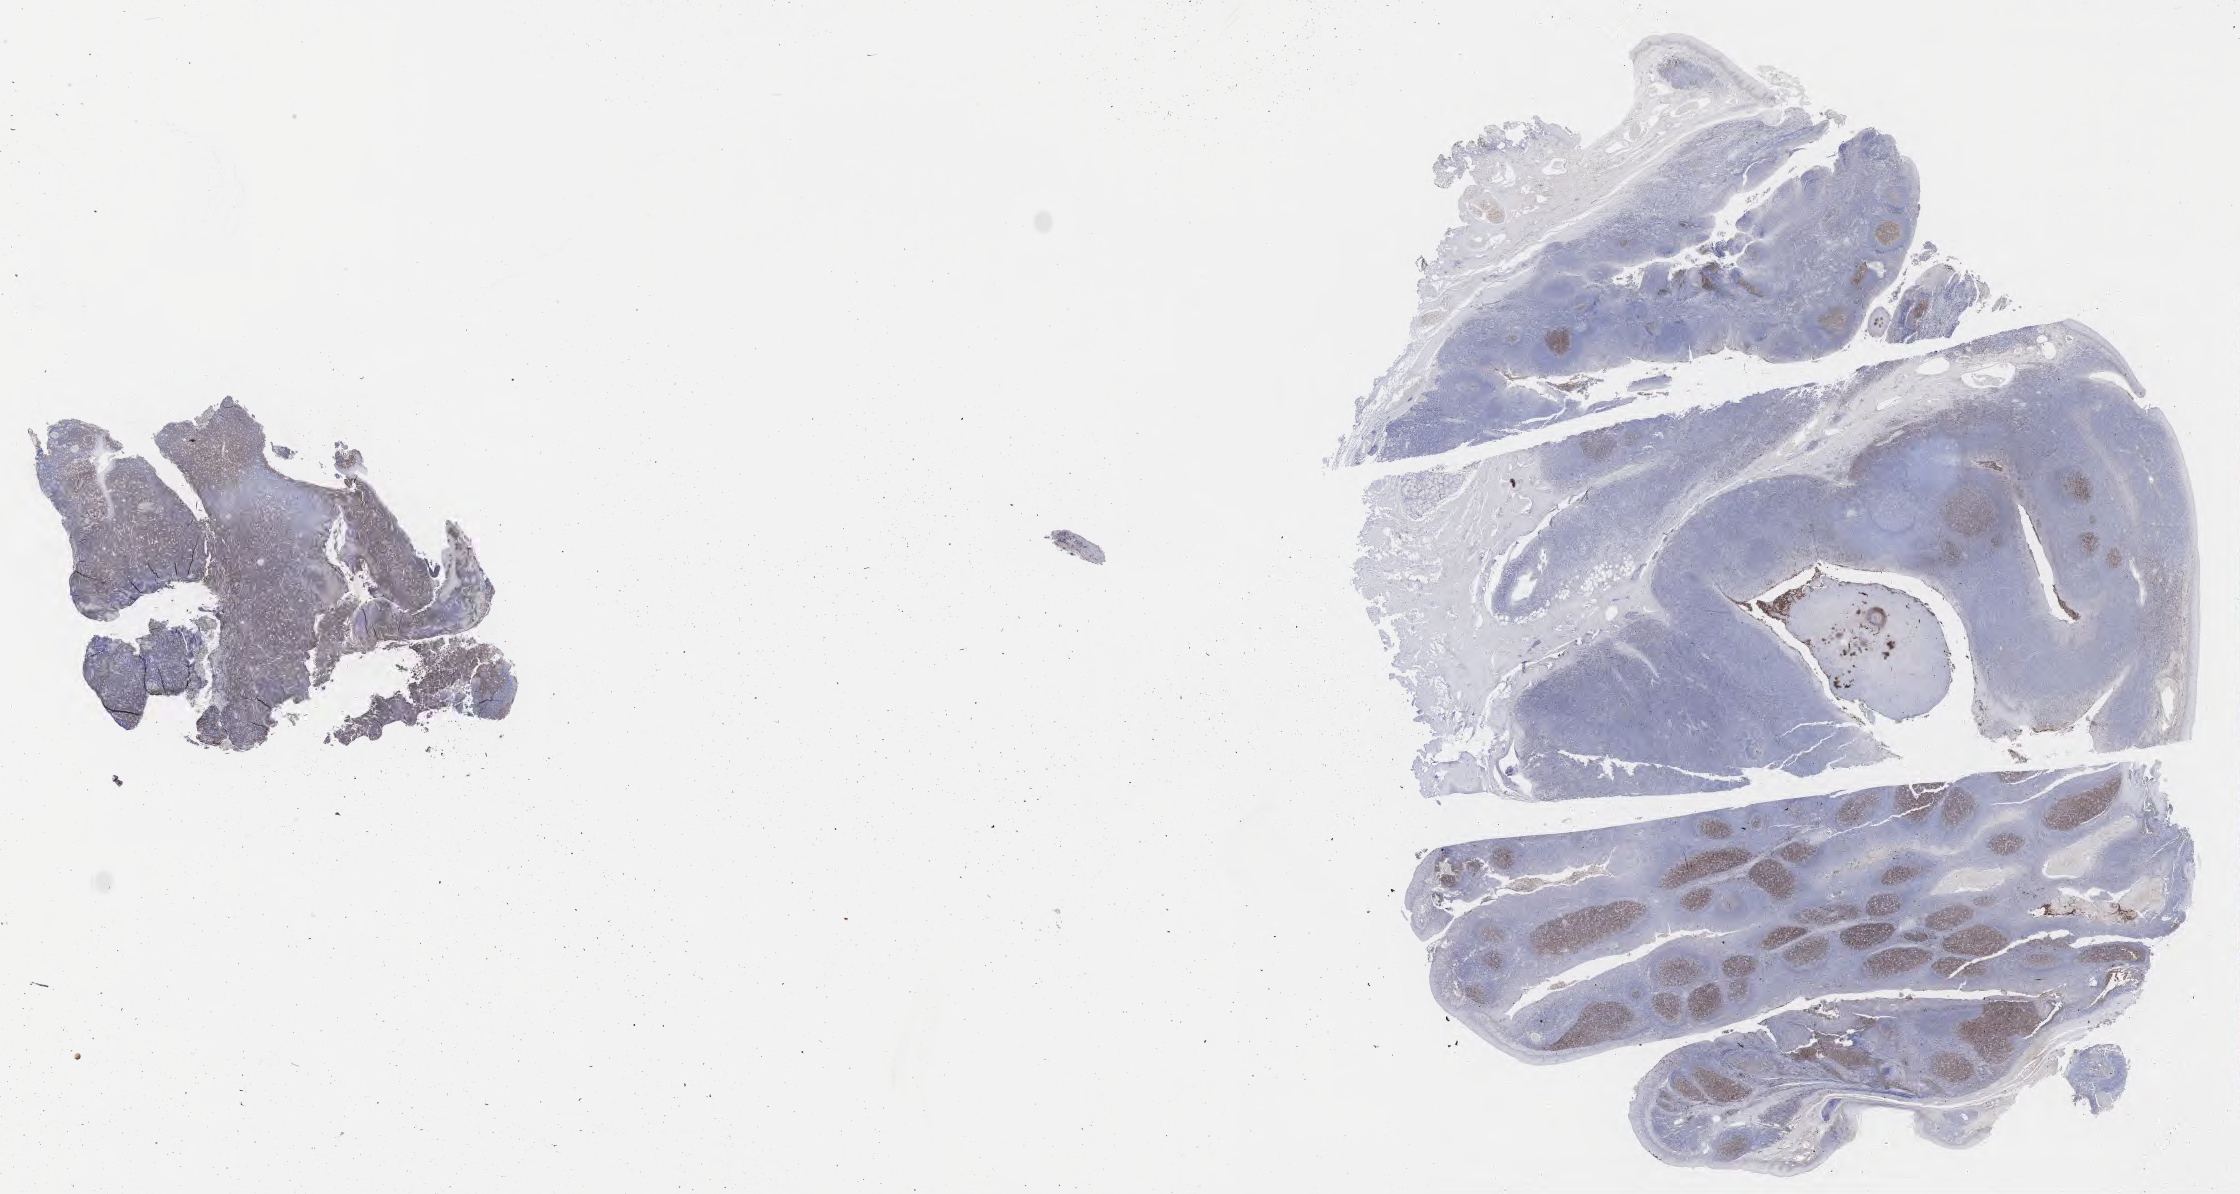
Immunohistochemistry (IHC) whole-slide image stained for CD10 — low-resolution overview of the scanned area, about 36.2 x 19.3 mm, specimen: tumor tissue. Patient: male, age at initial diagnosis 3 years.
Diagnosis: Burkitt lymphoma, NOS.